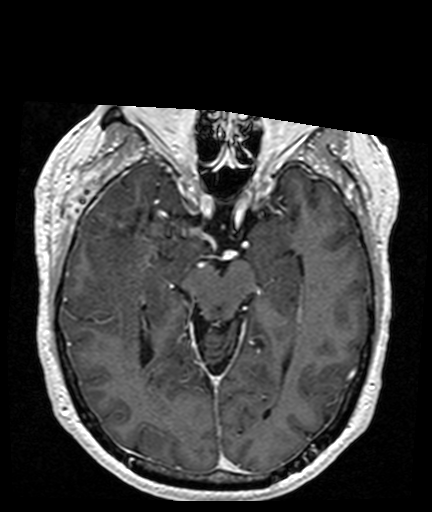
Brain MRI from a brain-tumour surgery series, one axial slice; position 102 of 176 along the scan axis; T1-weighted post-contrast; 1 mm slice thickness; 432 × 512 image matrix, field of view 194 × 230 mm. Case-level facts recorded for this patient, not image findings: histopathology: Glioblastoma; WHO grade: 4; IDH mutation: no.
Outlined on this slice (manually delineated by an expert):
- tumour: bounding box <118,221,125,228> (left, top, right, bottom; pixels)